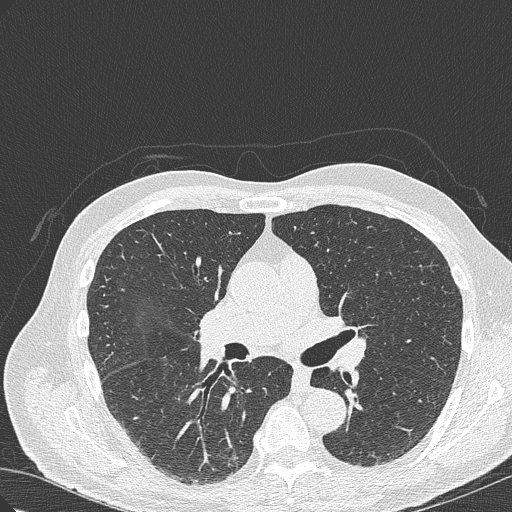
Low-dose screening chest CT, axial slice, baseline screening round, lung window (W 1500 / L -600 HU), lung (sharp) reconstruction kernel (B50f), 120 kVp, slice 136 of 322 in the series, 512 × 512 image matrix. Male participant, aged 70 years at enrolment. Current smoker at enrolment.
Lesion marked by an expert reader, bounding box [x1, y1, x2, y2] px = [199, 419, 262, 475]. The screening reader recorded 4 non-calcified nodules or masses ≥4 mm on this exam (right lower lobe, right lower lobe, right upper lobe, right lower lobe); which of them this box marks is not recorded. Official screen result: positive, change unspecified: nodule(s) >= 4 mm or enlarging nodule(s), mass(es), or other non-specific abnormalities suspicious for lung cancer. Participant outcome: lung cancer diagnosed 978 days after this screen (after the third annual screen) — bronchiolo-alveolar adenocarcinoma, NOS, right lower lobe, poorly differentiated (G3), stage IB (AJCC 6th edition), 30 mm at pathology.